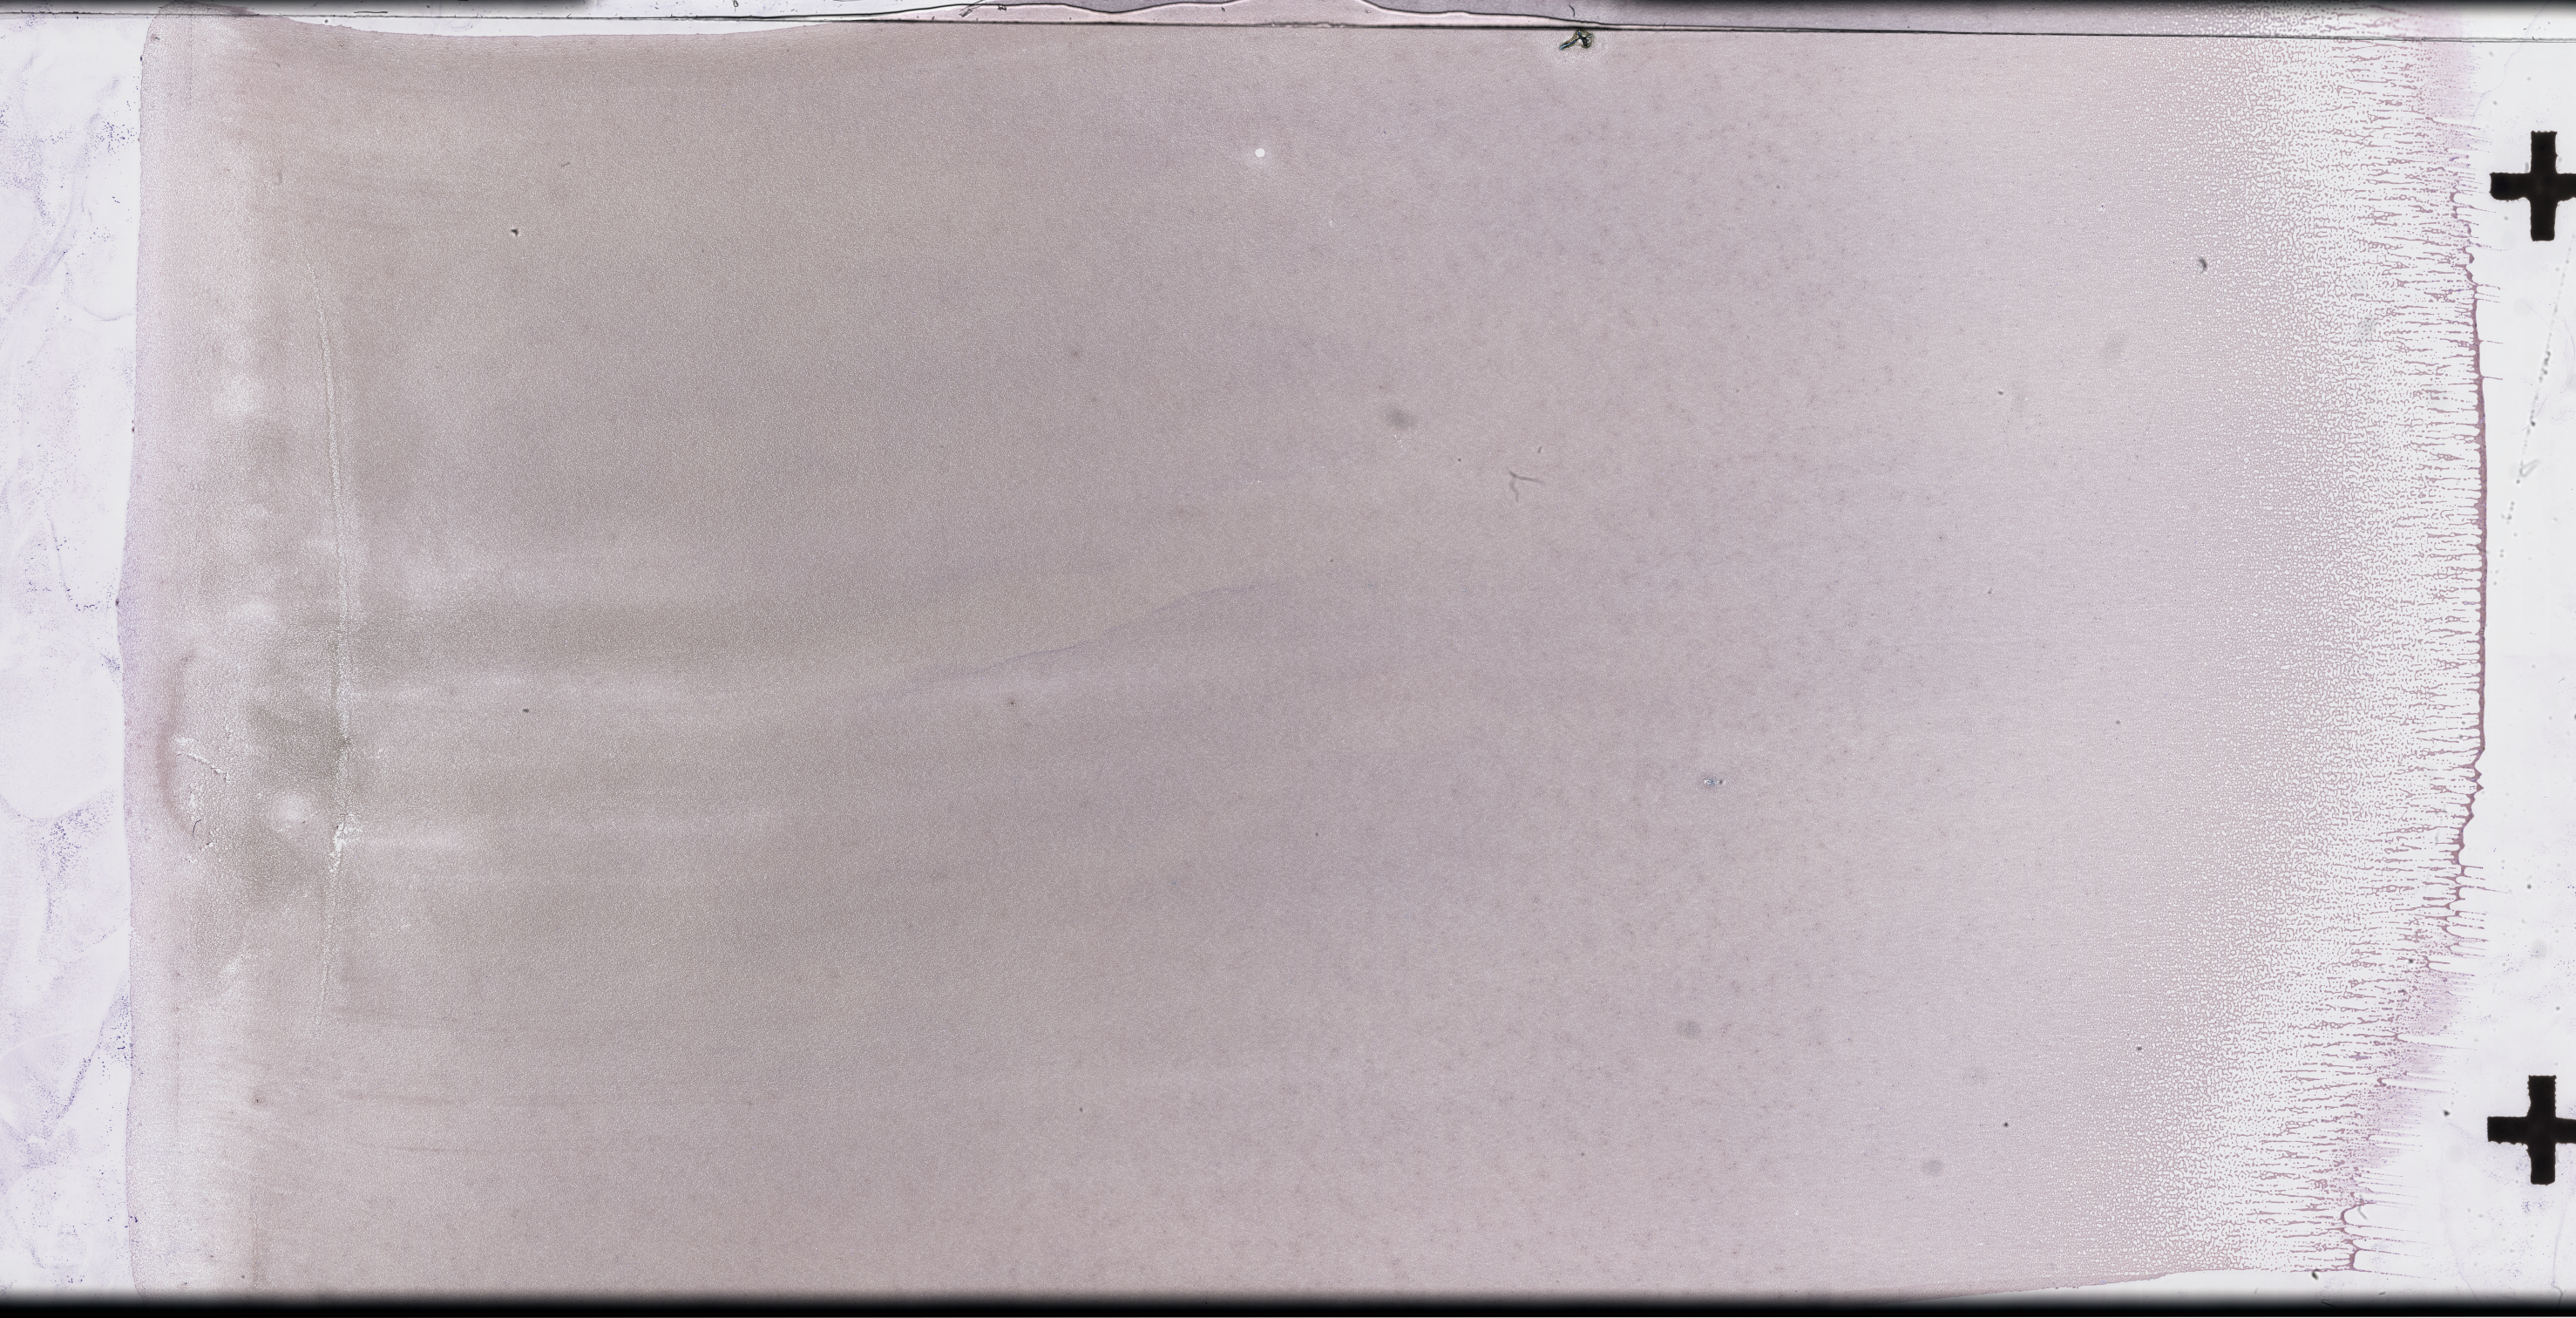
Whole-slide image of a whole blood smear, Wright–Giemsa stain — low-resolution overview of the scanned area, about 47.7 x 24.4 mm; EDTA-anticoagulated smear. Patient sex: male.
• from a patient with: Plasma Cell Myeloma